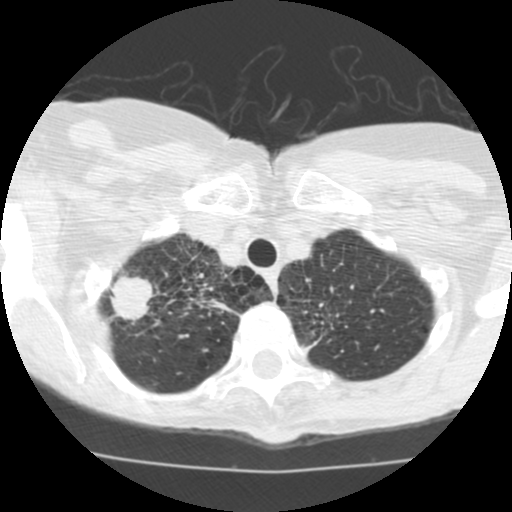
Low-dose screening chest CT, axial slice, second screening round (one year after baseline), lung window (W 1500 / L -600 HU), slice 15 of 115 in the series, 512 × 512 image matrix. Female participant, aged 68 years at enrolment.
Expert-annotated lung lesion, bounding box <98,265,161,335> (left, top, right, bottom; pixels). The screening reader recorded 3 non-calcified nodules or masses ≥4 mm on this exam (right upper lobe, right upper lobe, right middle lobe); which of them this box marks is not recorded. Later outcome: lung cancer diagnosed 36 days after this screen — large cell neuroendocrine carcinoma, right upper lobe, undifferentiated (G4), stage IB (AJCC 6th edition), 22 mm at pathology.